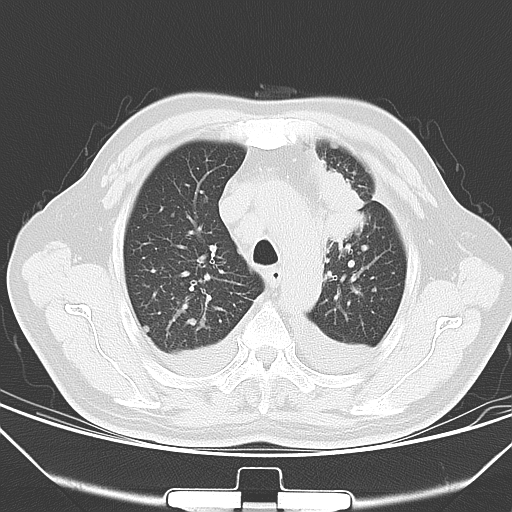
Chest CT, one axial slice. Slice 48 of 66 in the series (ordered by position). Lung window (W 1500 / L -600 HU). 5 mm slice thickness. 512 × 512 image matrix, field of view 352 × 352 mm. Patient: male, 66 years. From the clinical record (not read from this slice): clinical TNM (as recorded): T1c N0 M0.
Structures marked on this image (bounding box drawn by a radiologist):
- lung tumour (recorded histology: adenocarcinoma): bounding box <315,160,373,242> (left, top, right, bottom; pixels)